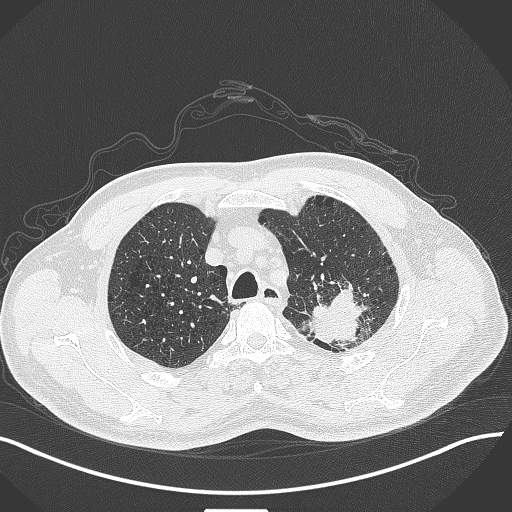
Chest CT, one axial slice; lung window (W 1500 / L -600 HU); 1 mm slice thickness; 512 × 512 image matrix, field of view 400 × 400 mm. Male patient, age 55 years. From the clinical record (not read from this slice): clinical TNM (as recorded): T3 N0 M1c; histopathological grade: G3.
Outlined on this slice (bounding box drawn by a radiologist):
- lung tumour (recorded histology: adenocarcinoma): bounding box [x1, y1, x2, y2] px = [308, 284, 380, 357]